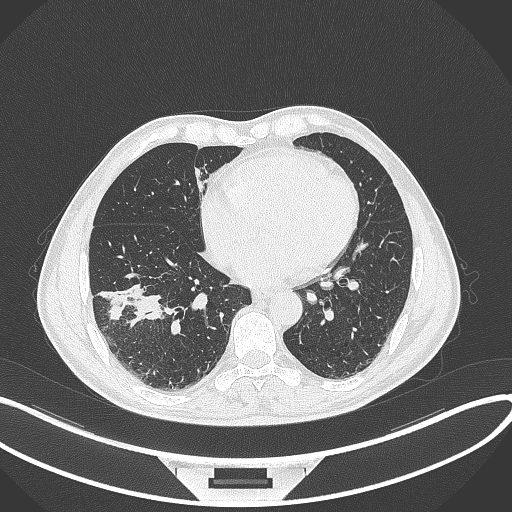
Chest CT, one axial slice. Slice 135 of 364 in the series (ordered by position). Reconstruction kernel B70f. Lung window (W 1500 / L -600 HU). 1 mm slice thickness. 512 × 512 image matrix, field of view 400 × 400 mm. Patient: male, 58 years. Case-level facts recorded for this patient, not image findings: clinical TNM (as recorded): T3 N0 M0.
Structures marked on this image (bounding box drawn by a radiologist):
- lung tumour (recorded histology: squamous cell carcinoma): box from (x=101, y=283) to (x=166, y=327) px